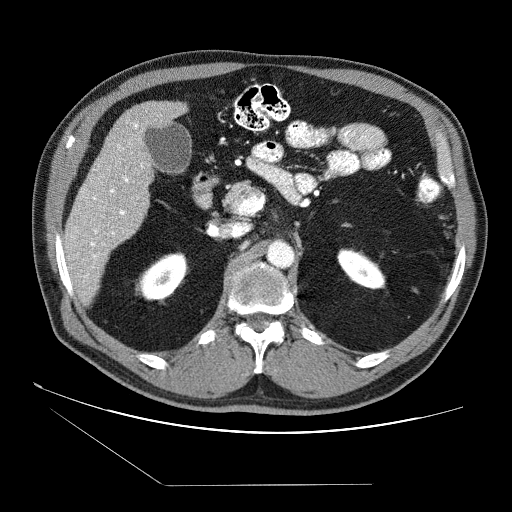
Contrast-enhanced abdominal CT (liver protocol), one axial slice. Position 30 of 87 along the scan axis. Reconstruction kernel STANDARD. 120 kVp. Soft-tissue window (W 400 / L 40 HU). 512 × 512 image matrix, field of view 400 × 400 mm. From the clinical record (not read from this slice): diagnosis: hepatocellular carcinoma (patient treated with transarterial chemoembolisation; whether this scan precedes or follows treatment is not stated here); TNM stage (as recorded): Stage-II; Child-Pugh class: B; tumour differentiation: no biopsy.
Outlined on this slice (semi-automatic segmentation, software-assisted and operator-edited):
- liver parenchyma outside the tumour (the mass and vessels are separate outlines, so this box may not span the whole liver): bounding box <64,101,186,299> (left, top, right, bottom; pixels)
- liver vessels: <72,123,143,278>